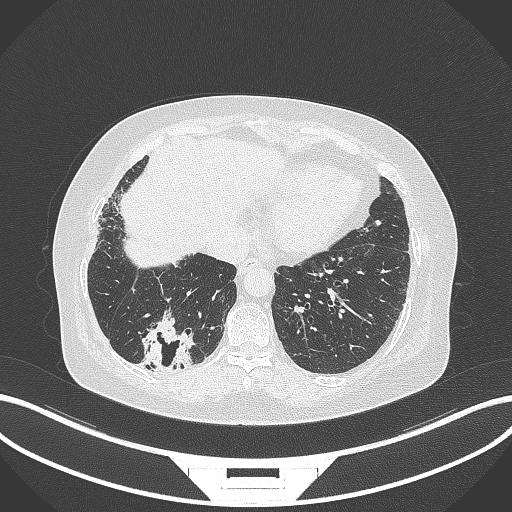
Chest CT, one axial slice. 120 kVp. Lung window (W 1500 / L -600 HU). 1 mm slice thickness. 512 × 512 image matrix, field of view 400 × 400 mm. Patient: female, 65 years. Case-level facts recorded for this patient, not image findings: clinical TNM (as recorded): T2b N1 M0.
Structures marked on this image (bounding box drawn by a radiologist):
- lung tumour (recorded histology: adenocarcinoma): box from (x=140, y=312) to (x=196, y=374) px